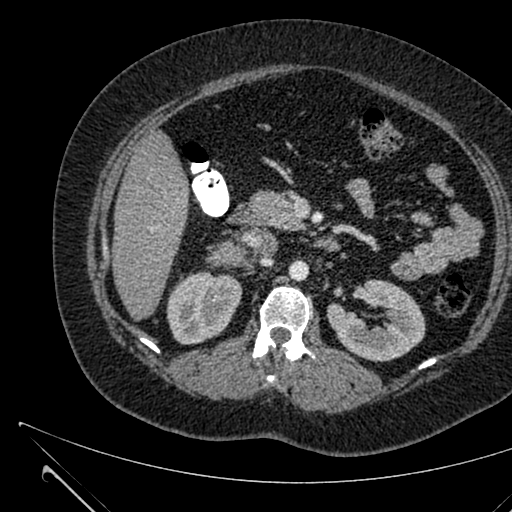
Contrast-enhanced abdominal CT, one axial slice. Slice 352 of 731 in the series (ordered by position). 120 kVp. Soft-tissue window (W 400 / L 40 HU). 512 × 512 image matrix. Patient: female, 36 years. From the clinical record (not read from this slice): diagnosis: adrenocortical carcinoma; tumour side: right adrenal; tumour size at pathology: 10 cm; Ki-67 index: 20 %; stage (as recorded): 4.
Outlined on this slice (semi-automatically segmented with operator editing):
- mass: bounding box <217,242,246,266> (left, top, right, bottom; pixels)